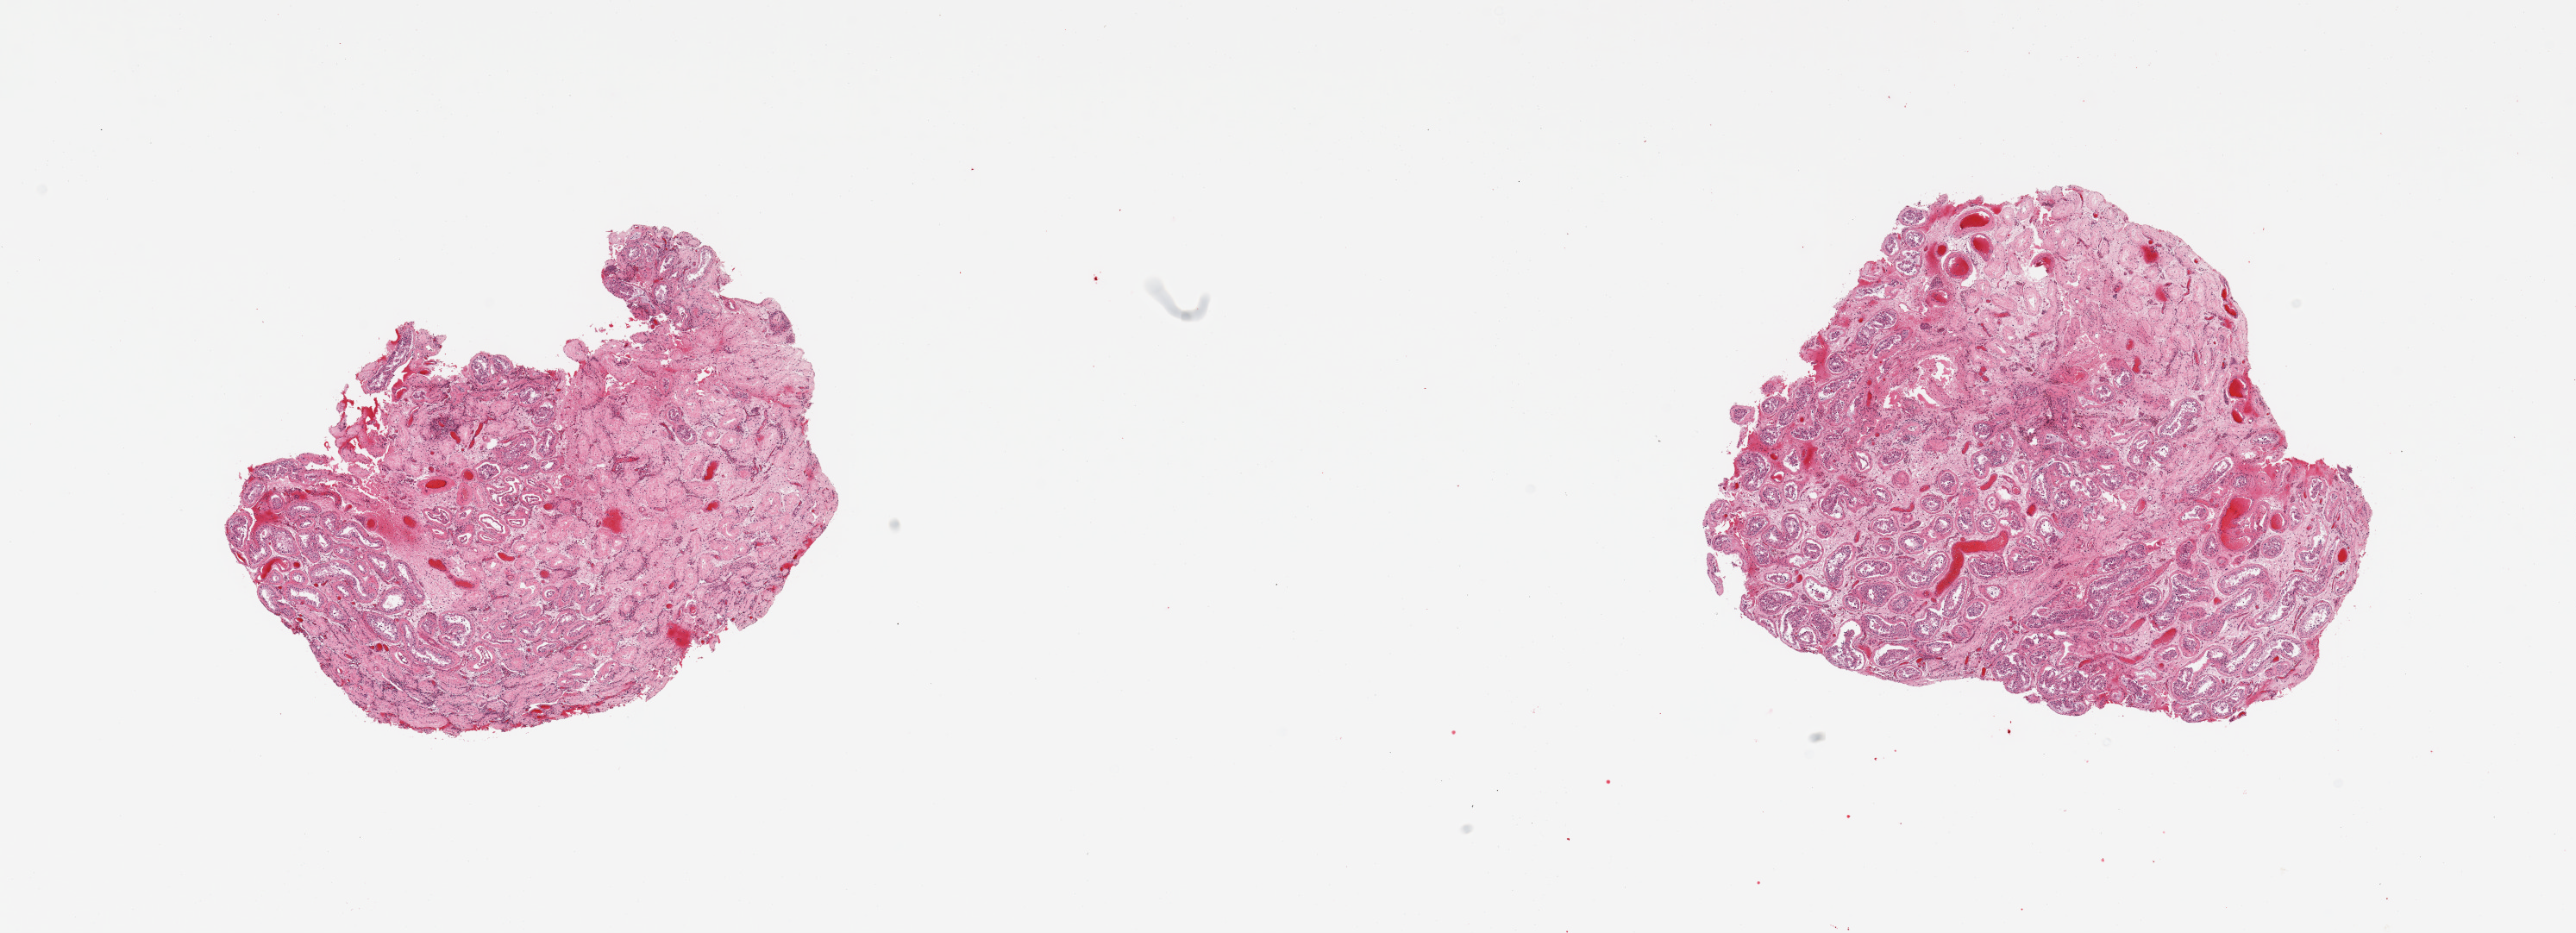
Digitized H&E-stained section, brightfield — a low-resolution overview of the entire scanned area, about 23.6 x 8.6 mm (slide scanned at 20x). PAXgene-fixed paraffin-embedded (PFPE) section. Sampled site (target tissue): testis. Tissue donor sample.
• pathologist's review note for this sample: 2 pieces; extensively hyalinized, minimal spermatogenesis